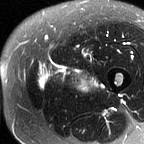
MRI of an extremity soft-tissue mass, one axial slice. T2-weighted fat-saturated. MR volume resampled by the dataset authors to the PET/CT grid (not the native acquisition matrix). 3.27 mm slice thickness. 144 × 144 image matrix. Female patient. From the clinical record (not read from this slice): histological type: pleiomorphic leiomyosarcoma; grade: intermediate; site of the primary tumour: left thigh.
Structures marked on this image (expert contour drawn on MRI and transferred to this co-registered scan by the dataset authors):
- gross tumour volume including surrounding oedema: box from (x=38, y=60) to (x=101, y=93) px